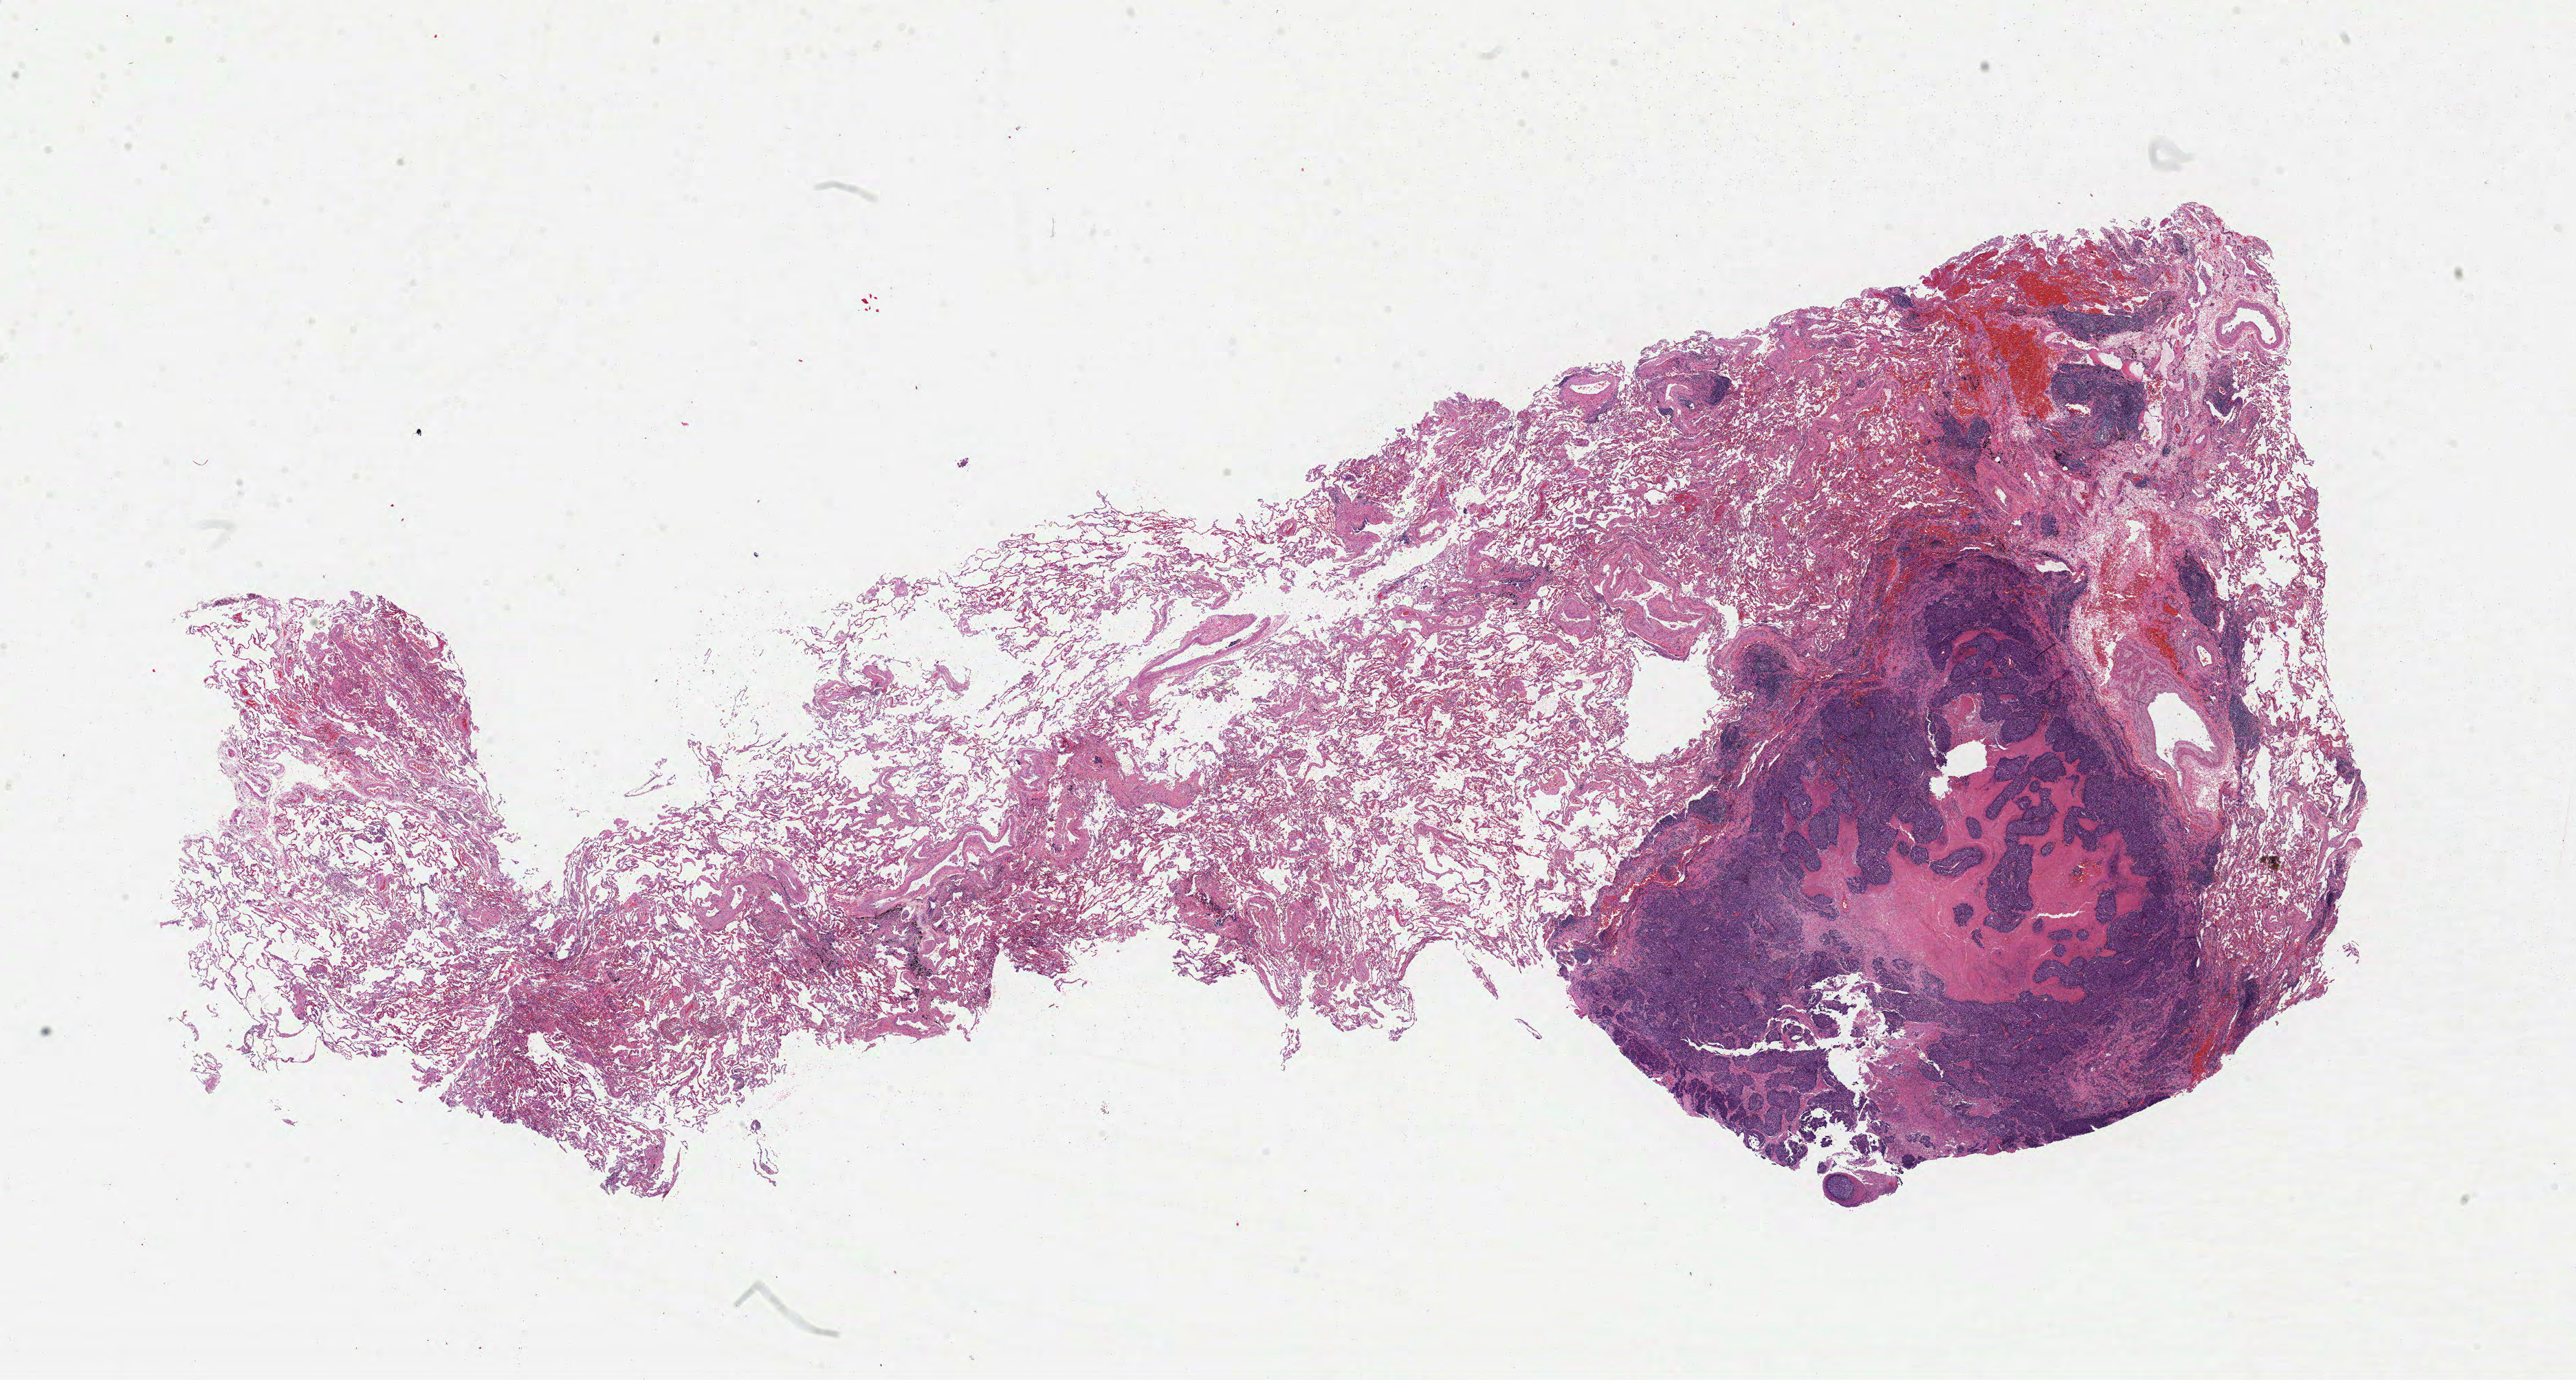
Hematoxylin and eosin (H&E) stained whole-slide image — low-resolution overview of the scanned area, about 30.2 x 16.2 mm, formalin-fixed paraffin-embedded (FFPE) diagnostic section, lung, primary tumour sample. Patient: female, age at initial diagnosis 61 years.
Histologic diagnosis: Squamous cell carcinoma, NOS (lower lobe, lung). Laterality: left. TNM: T2 N0 M1. AJCC pathologic stage: IV (7th edition).